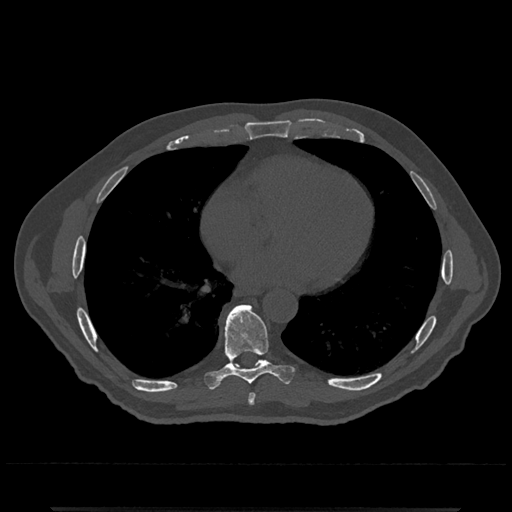
CT including the spine, one axial slice. Slice 667 of 797 in the series (ordered by position). Reconstruction kernel Br40s/3. Bone window (W 1800 / L 400 HU). 0.5 mm slice thickness. 512 × 512 image matrix. Male patient, age 67 years. Case-level facts recorded for this patient, not image findings: primary cancer: prostate.
Structures marked on this image (semi-automatically segmented with operator editing):
- T7 vertebra: bounding box [x1, y1, x2, y2] px = [248, 393, 256, 405]
- T8 vertebra: [204, 304, 294, 389]